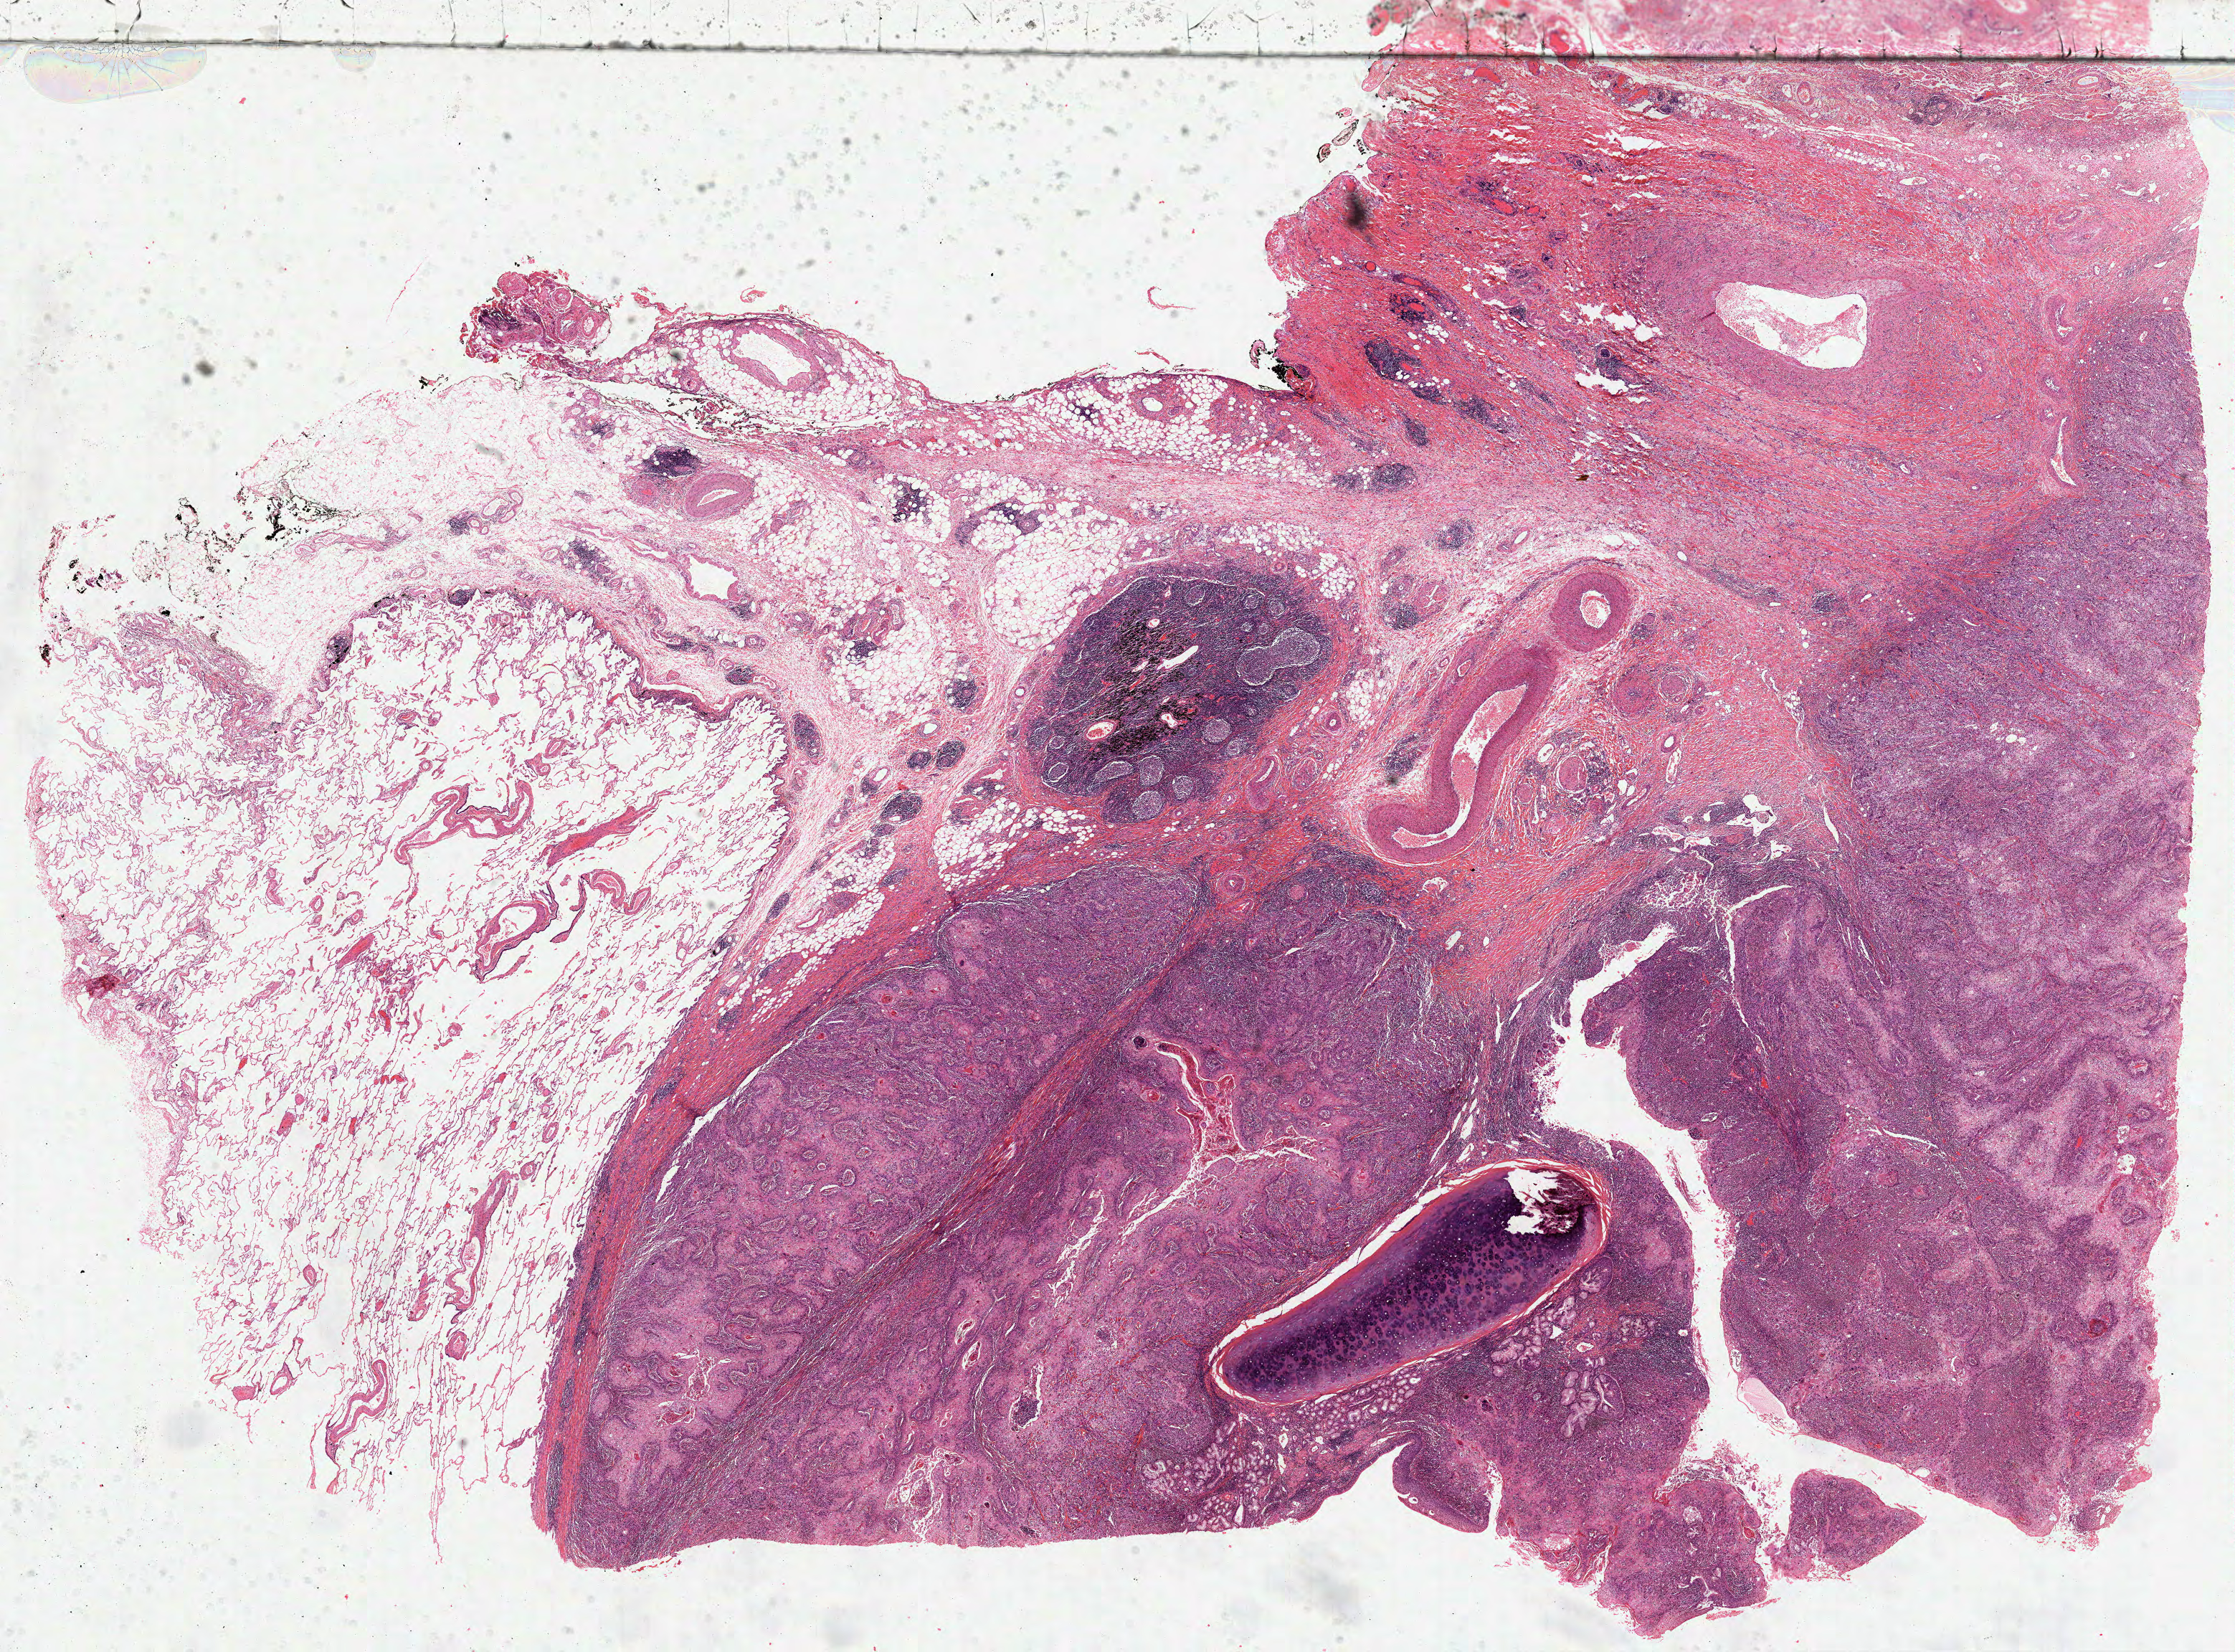
Digitized H&E tissue section (whole slide), a low-resolution overview of the entire scanned area, about 25.1 x 18.6 mm (slide scanned at 40x), formalin-fixed paraffin-embedded (FFPE) diagnostic section, sample: primary tumour, lung. Male patient; age at initial diagnosis 70 years.
AJCC pathologic stage: IB (6th edition). Diagnosis: Squamous cell carcinoma, NOS (upper lobe, lung).